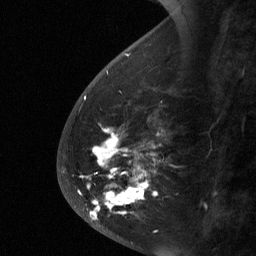
Breast MRI (dynamic contrast-enhanced), one sagittal slice; position 21 of 64 along the scan axis; dynamic contrast-enhanced study with each time point stored as its own series, time point 2 of 3 at this slice position (early post-contrast, ordered by acquisition time); 1.5 T; TE 4.8 ms, TR 27 ms; 2 mm slice thickness; 256 × 256 image matrix, field of view 180 × 180 mm. Patient: female, 56 years. From the clinical record (not read from this slice): setting: breast cancer imaged before/during neoadjuvant chemotherapy; receptor status: HER2-positive.
Structures marked on this image (semi-automatically segmented with operator editing):
- analysis volume of interest (the breast-tissue region the enhancement analysis was run in; not a lesion): bounding box <59,104,171,229> (left, top, right, bottom; pixels)
- tumour enhancement mask (voxels above the 90 % enhancement threshold inside the analysis volume of interest): <89,130,157,220>